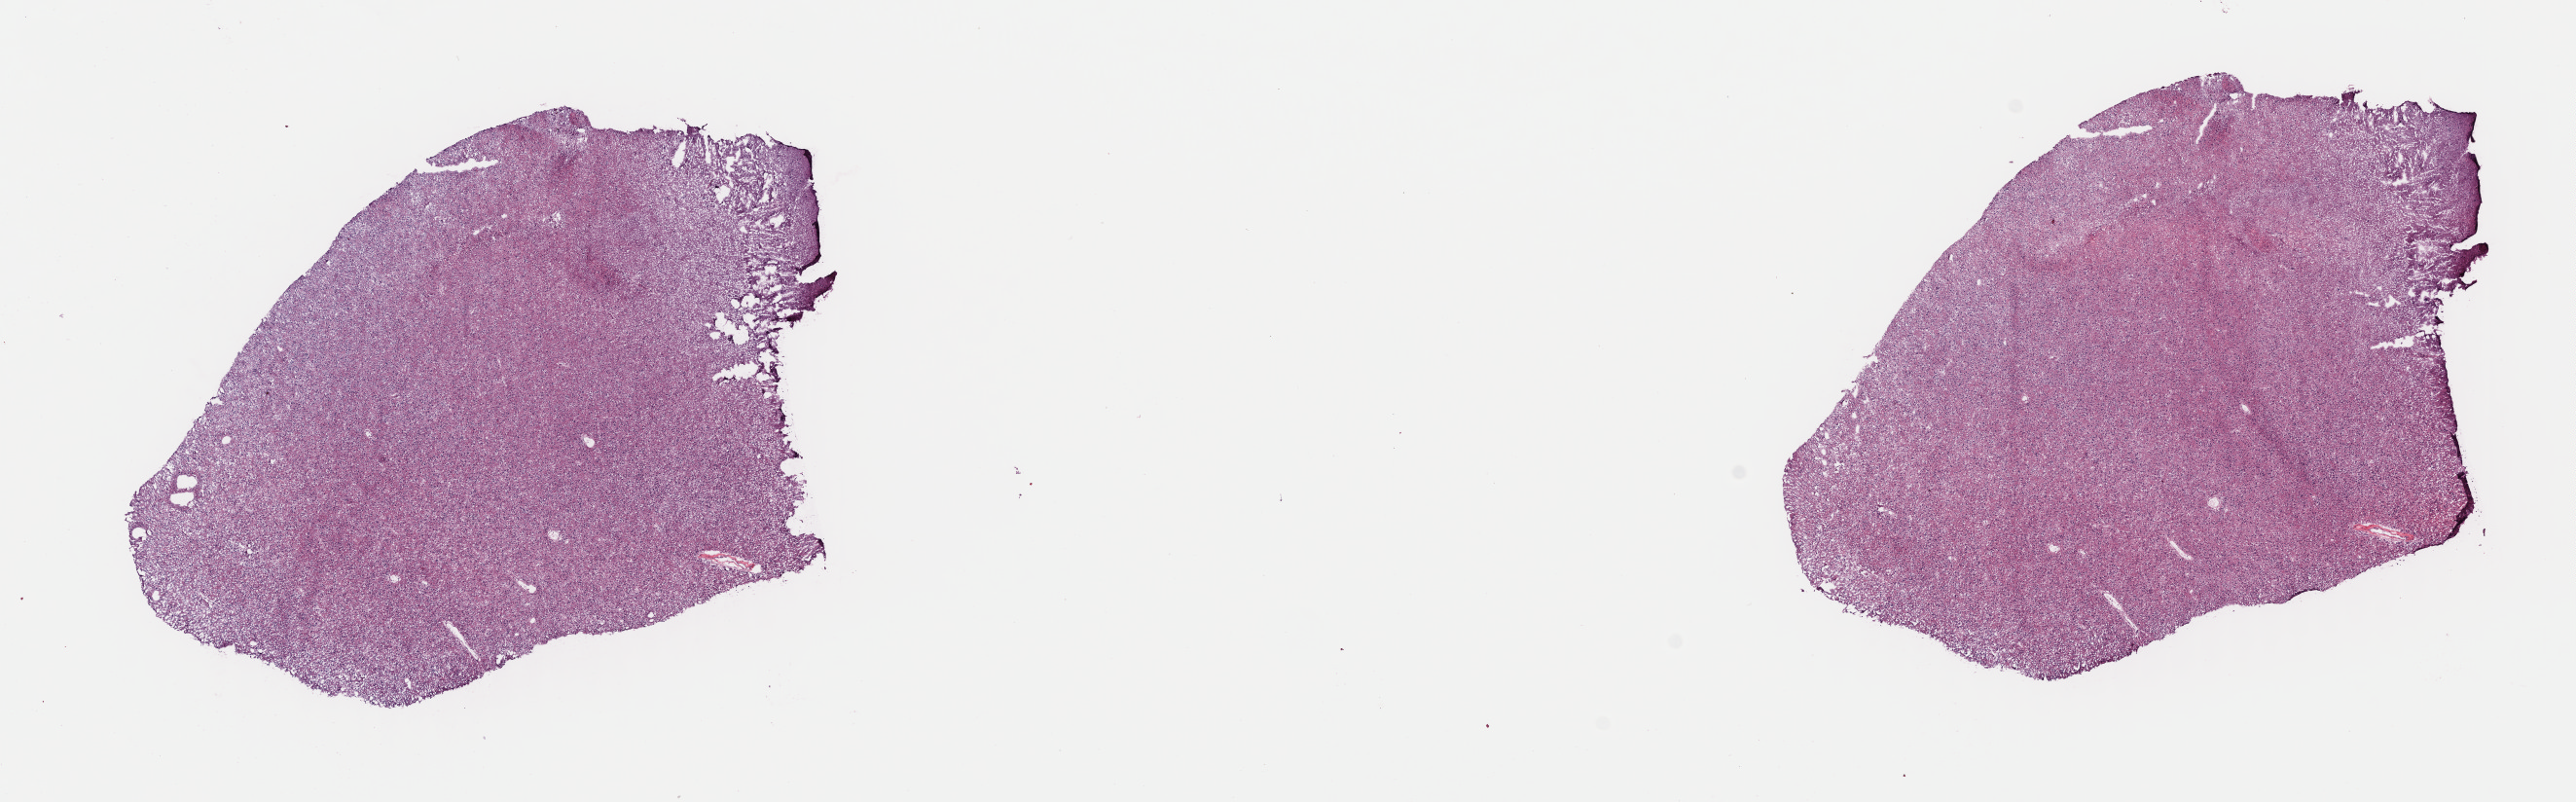
H&E-stained whole-slide image, whole scanned area (about 20.9 x 6.5 mm) shown as a low-resolution overview. Frozen section from the top of the tissue portion. Sample: primary tumour, brain. Male, age 52 years at initial diagnosis. Histologic grade: G2 (moderately differentiated). Pathologist review of this section (percent, as recorded): tumour cells 40%, tumour nuclei 80%, normal cells 10%, stromal cells 50%, necrosis 0%. Infiltration values recorded for this section: lymphocyte infiltration 0%, monocyte infiltration 0%, neutrophil infiltration 0%.
Diagnosis: Oligodendroglioma, NOS. Laterality: right.